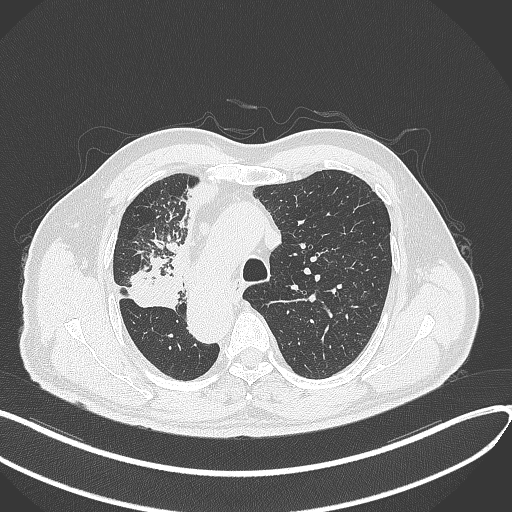
Chest CT, one axial slice. Position 229 of 300 along the scan axis. Lung window (W 1500 / L -600 HU). 512 × 512 image matrix, field of view 400 × 400 mm. Male patient, age 67 years. From the clinical record (not read from this slice): clinical TNM (as recorded): T2a N0 M0.
Structures marked on this image (rectangle marked by the reading radiologist):
- lung tumour (recorded histology: squamous cell carcinoma): box from (x=127, y=249) to (x=184, y=309) px